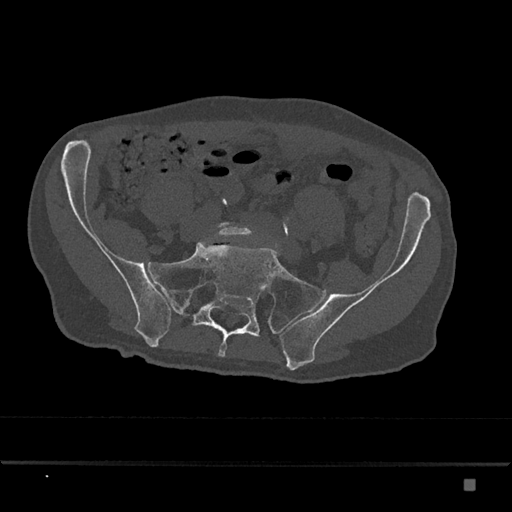
CT including the spine, one axial slice. Slice 209 of 797 in the series (ordered by position). Reconstruction kernel Br40s/3. 120 kVp. Bone window (W 1800 / L 400 HU). 0.5 mm slice thickness. 512 × 512 image matrix, field of view 390 × 390 mm. Patient: male, 72 years. From the clinical record (not read from this slice): primary cancer: prostate.
Outlined on this slice (semi-automatically segmented with operator editing):
- L5 vertebra: bounding box <217,222,254,237> (left, top, right, bottom; pixels)